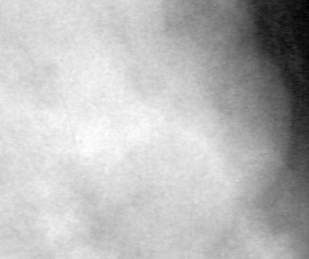
Region of interest cut from a scanned film mammogram (one marked finding); right breast; MLO view; BI-RADS breast density category 3 (scale 1–4).
Marked abnormality: mass, shape lobulated, margins obscured; BI-RADS assessment category 4; pathology result (as recorded, not read from the image): benign.